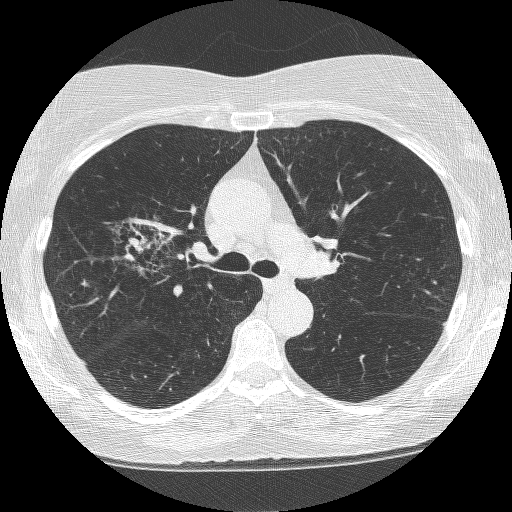
Chest CT (low-dose screening protocol), one axial image. Second annual screen. Lung window (W 1500 / L -600 HU). Slice 160 of 249 in the series. 512 × 512 image matrix. Female participant, aged 64 years at enrolment. Former smoker at enrolment.
• Expert-annotated lung lesion, bounding box (x1, y1, x2, y2) in pixels: (115, 205, 208, 293).
• The screening reader recorded 4 non-calcified nodules or masses ≥4 mm on this exam (right upper lobe, right upper lobe, right upper lobe, left upper lobe); which of them this box marks is not recorded.
• Official screen result: positive, other.
• Participant outcome: lung cancer diagnosed 381 days after this screen — adenocarcinoma, NOS, right upper lobe, right middle lobe, right hilum, stage IV (AJCC 6th edition), 85 mm at pathology.